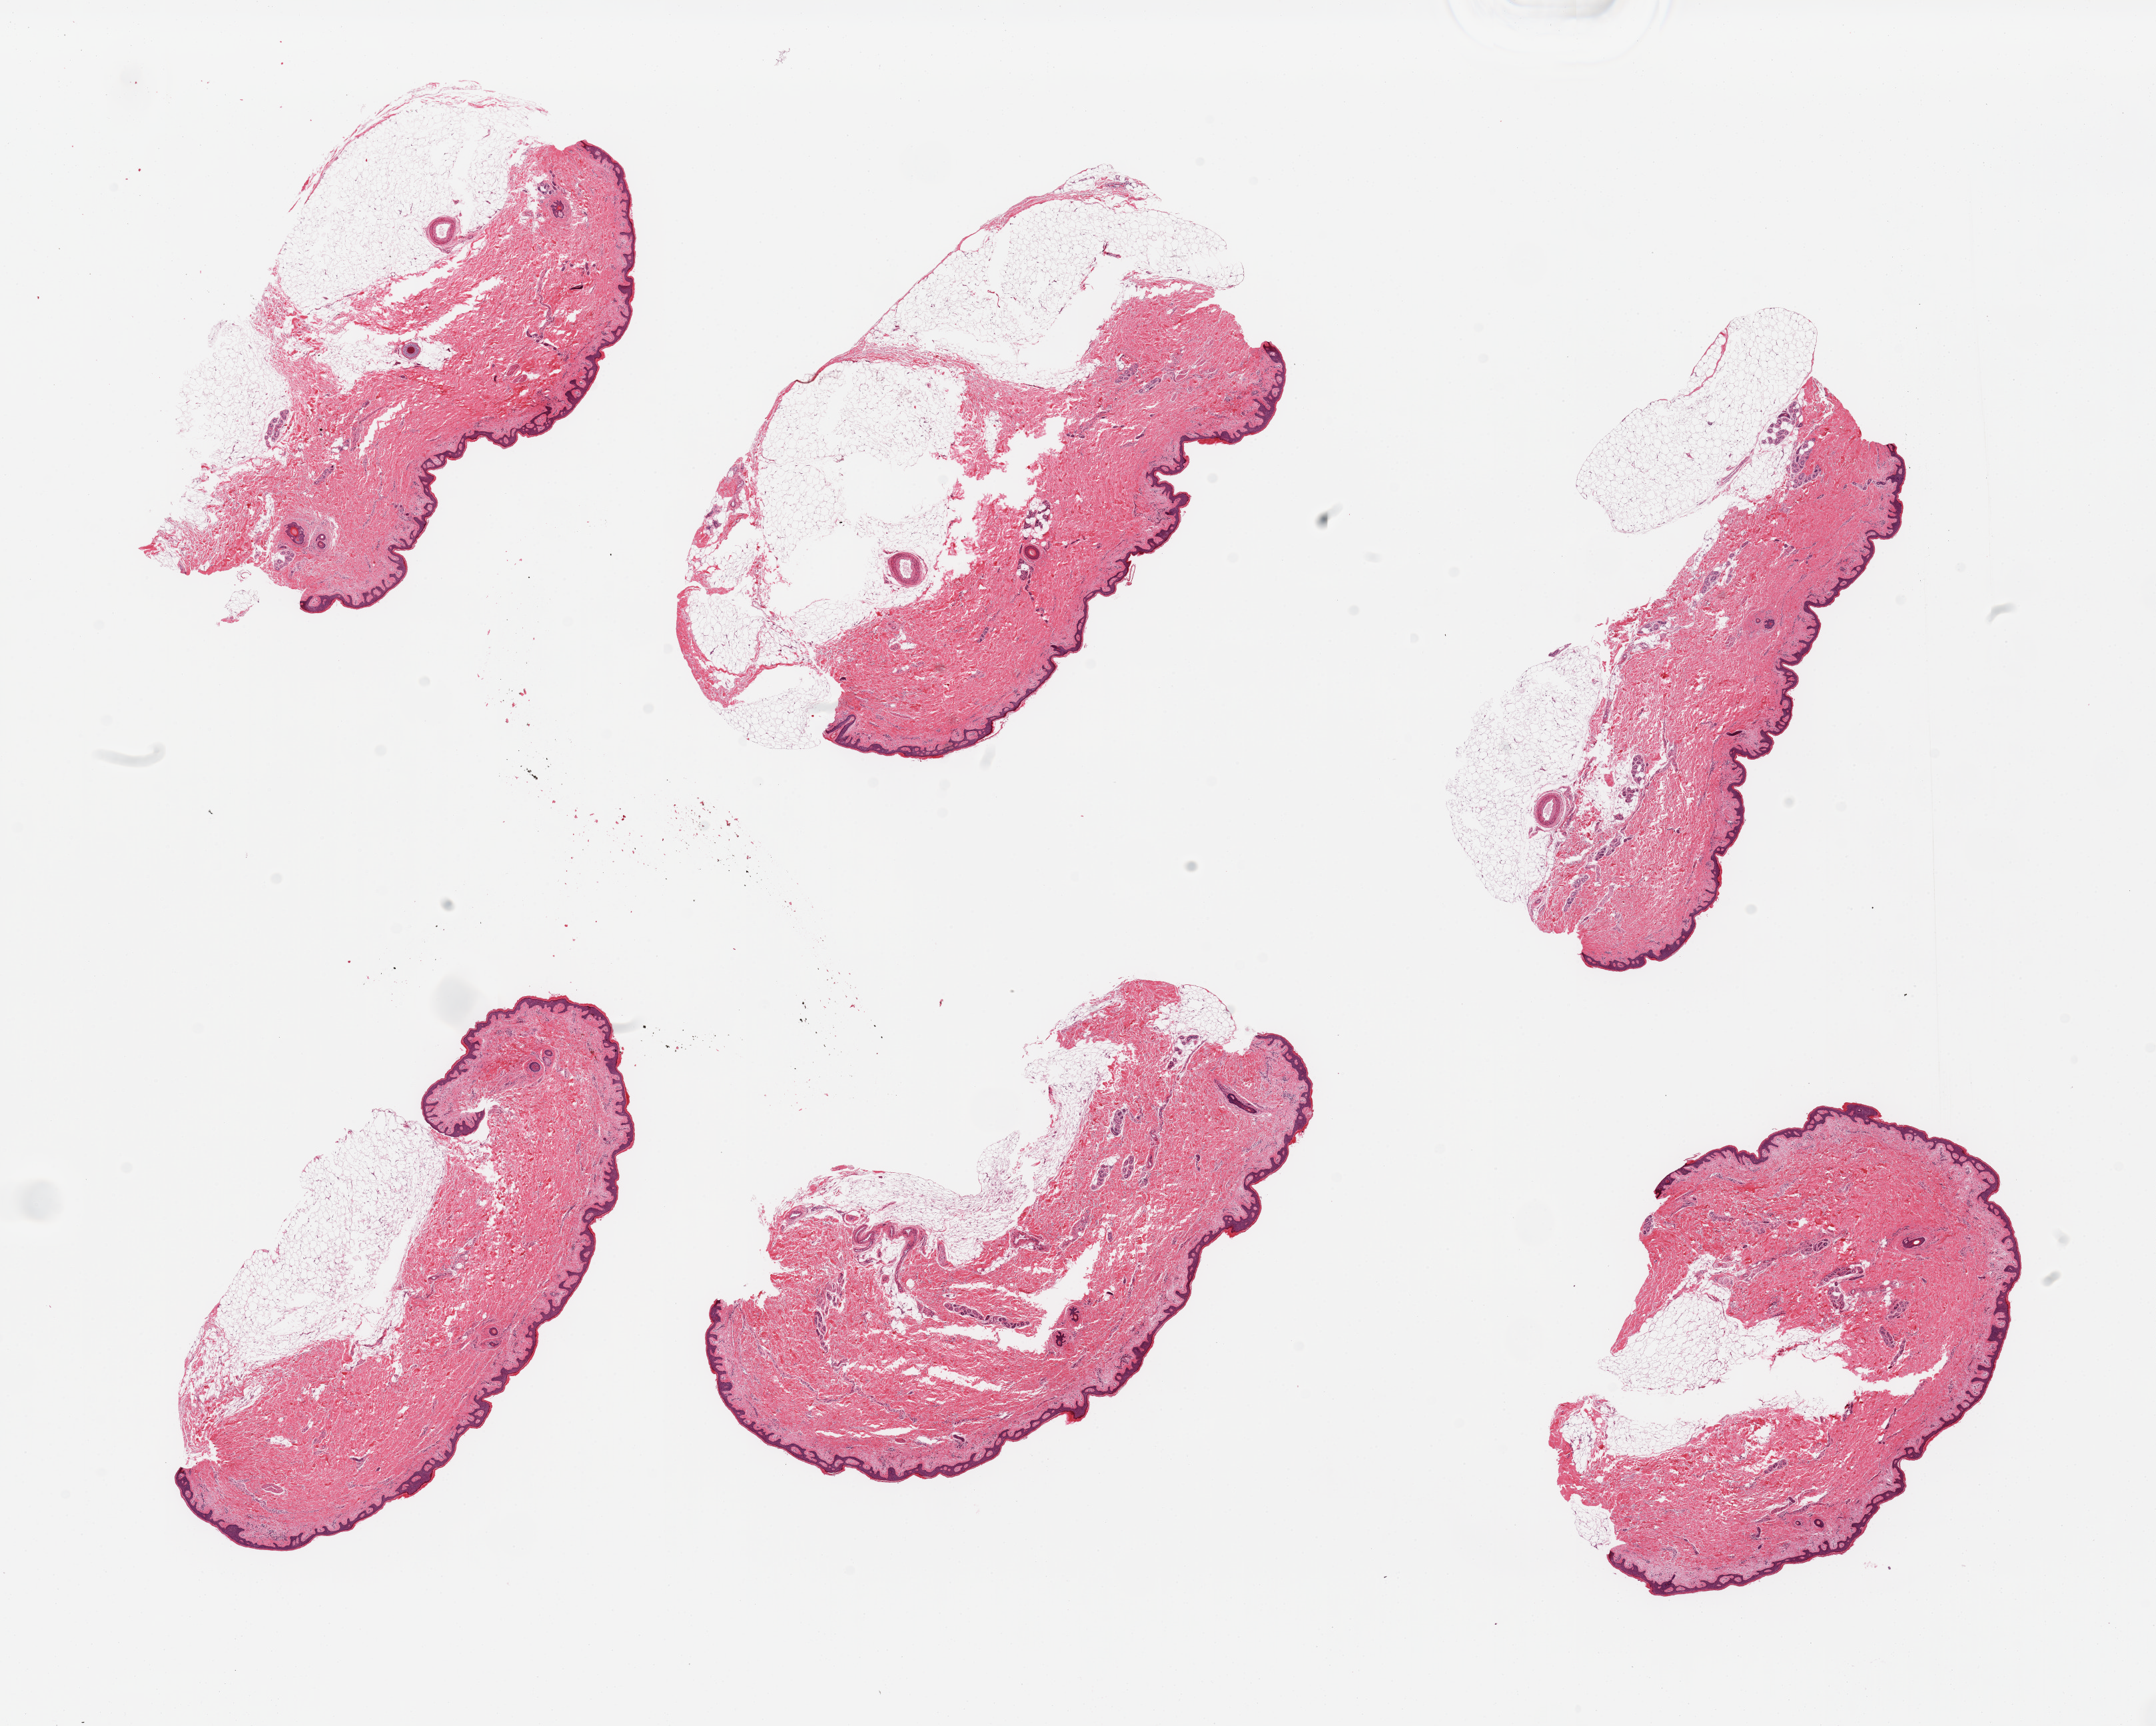
Digitized hematoxylin and eosin (H&E)-stained section — low-resolution overview of the scanned area, about 25.6 x 20.5 mm, PAXgene-fixed, paraffin-embedded tissue, section of skin of suprapubic region (target tissue), donor tissue sample. Donor sex: male.
- pathologist's review note for this sample: 6 pieces, squamous epithelium is ~40 microns; subcutaneous adherent fat up to ~2.5mm